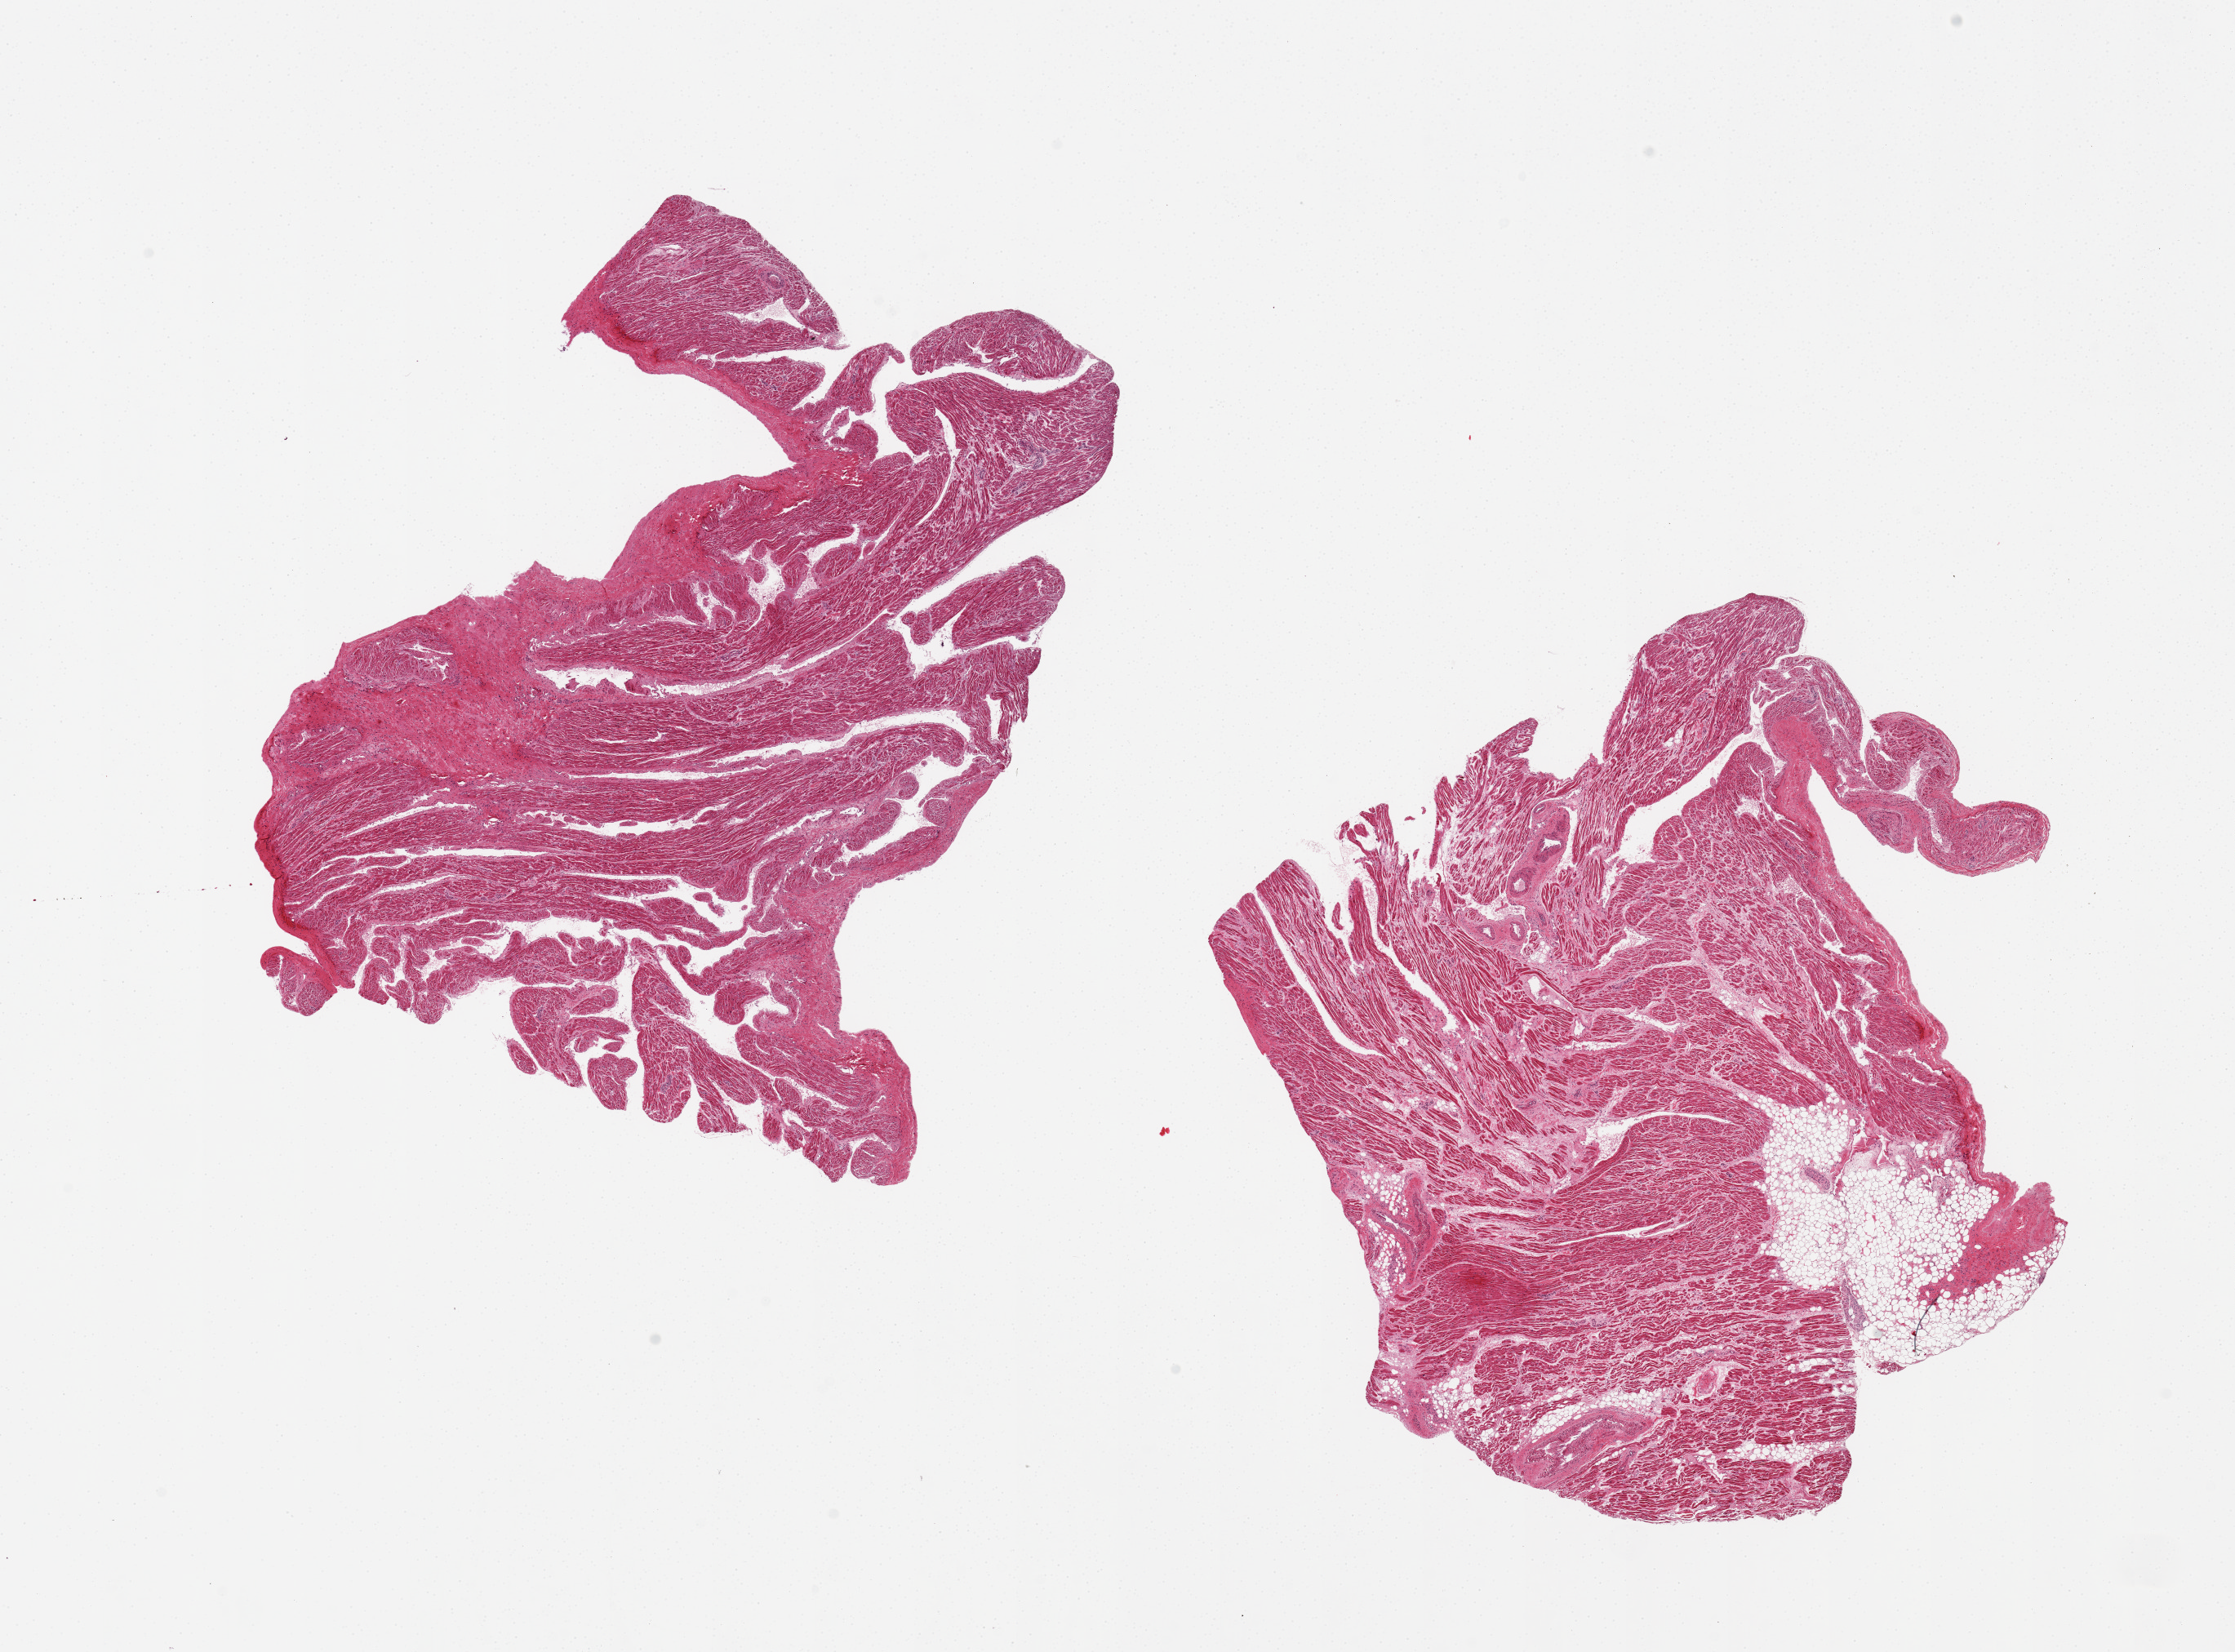
Whole-slide image, hematoxylin and eosin (H&E) stain, brightfield, whole scanned area (about 21.7 x 16.0 mm, acquisition: 20x scan) shown as a low-resolution overview. PAXgene-fixed paraffin-embedded (PFPE) section. Section of auricular appendage (target tissue). Tissue donor sample.
Reviewer comment on this tissue sample: 2 pieces, adherent fatty nubbin on one, ~ 3mm.